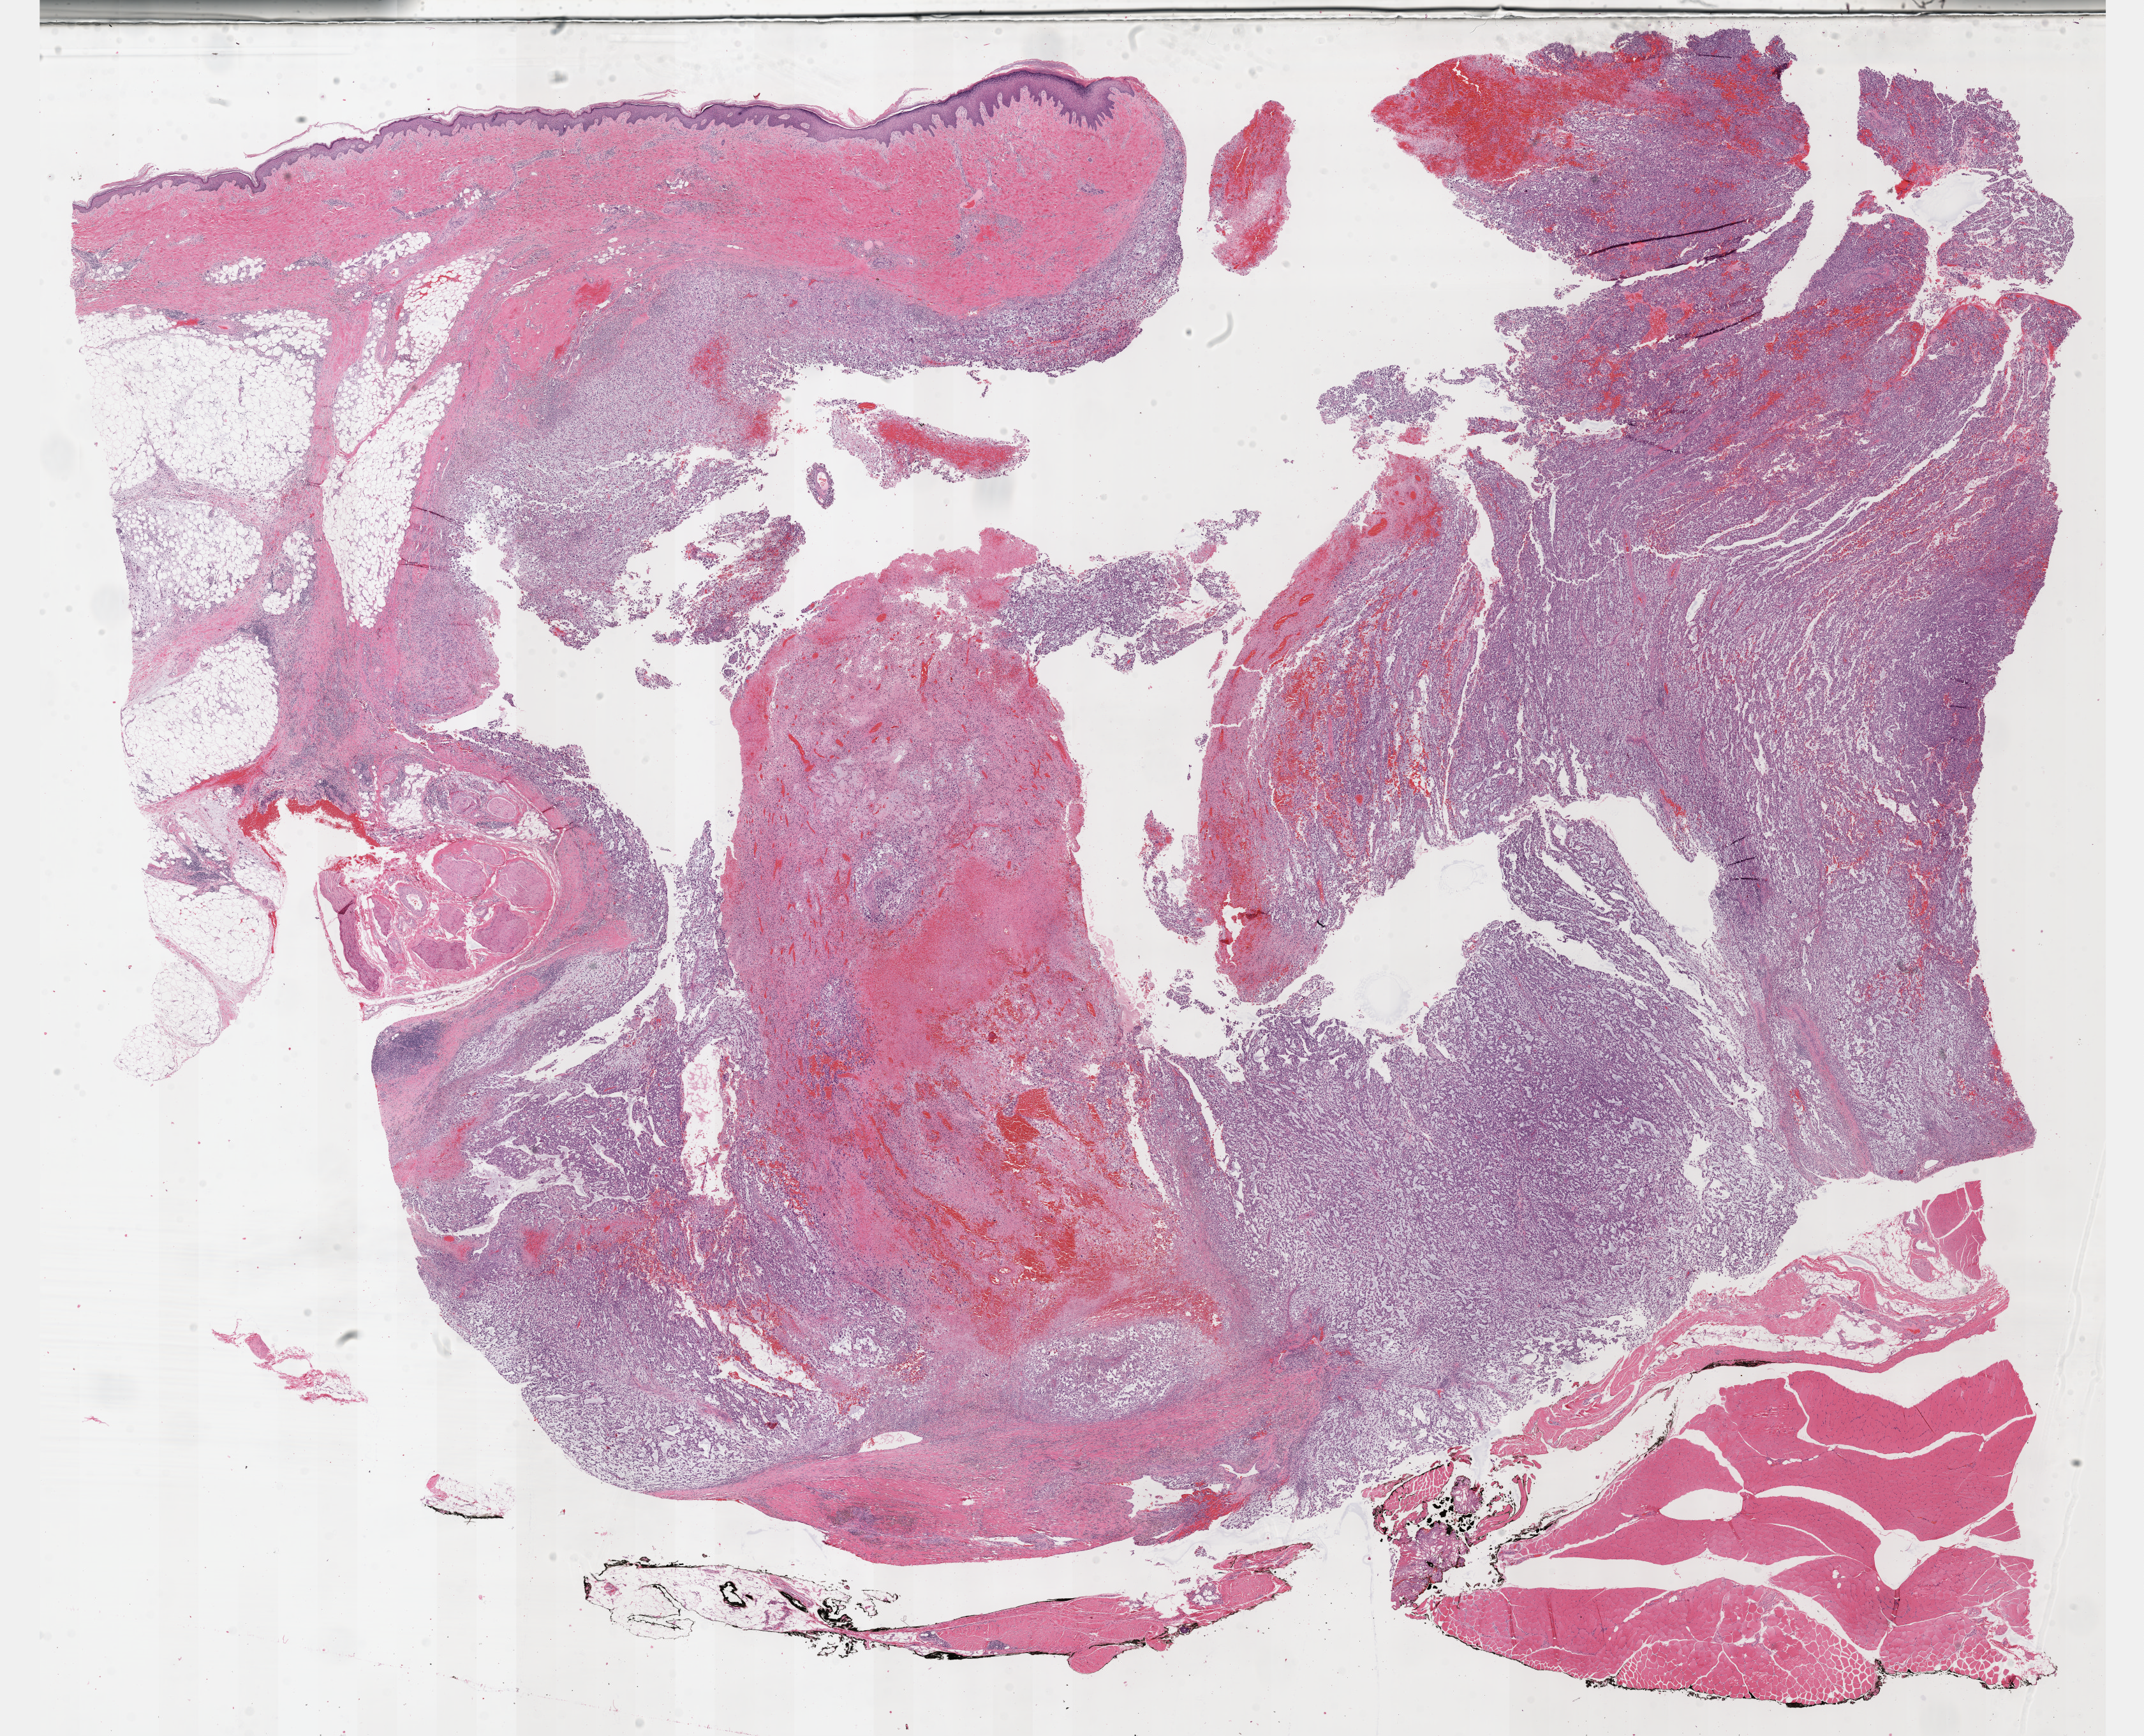
Whole-slide histology image, Hematoxylin and eosin (H&E) stained — low-resolution overview of the scanned area, about 27.2 x 22.0 mm (acquisition: 40x scan), formalin-fixed paraffin-embedded (FFPE) diagnostic section, connective, subcutaneous and other soft tissues, primary tumour sample. Patient: female, age at initial diagnosis 59 years.
• histologic diagnosis: Fibromyxosarcoma (connective, subcutaneous and other soft tissues of lower limb and hip)